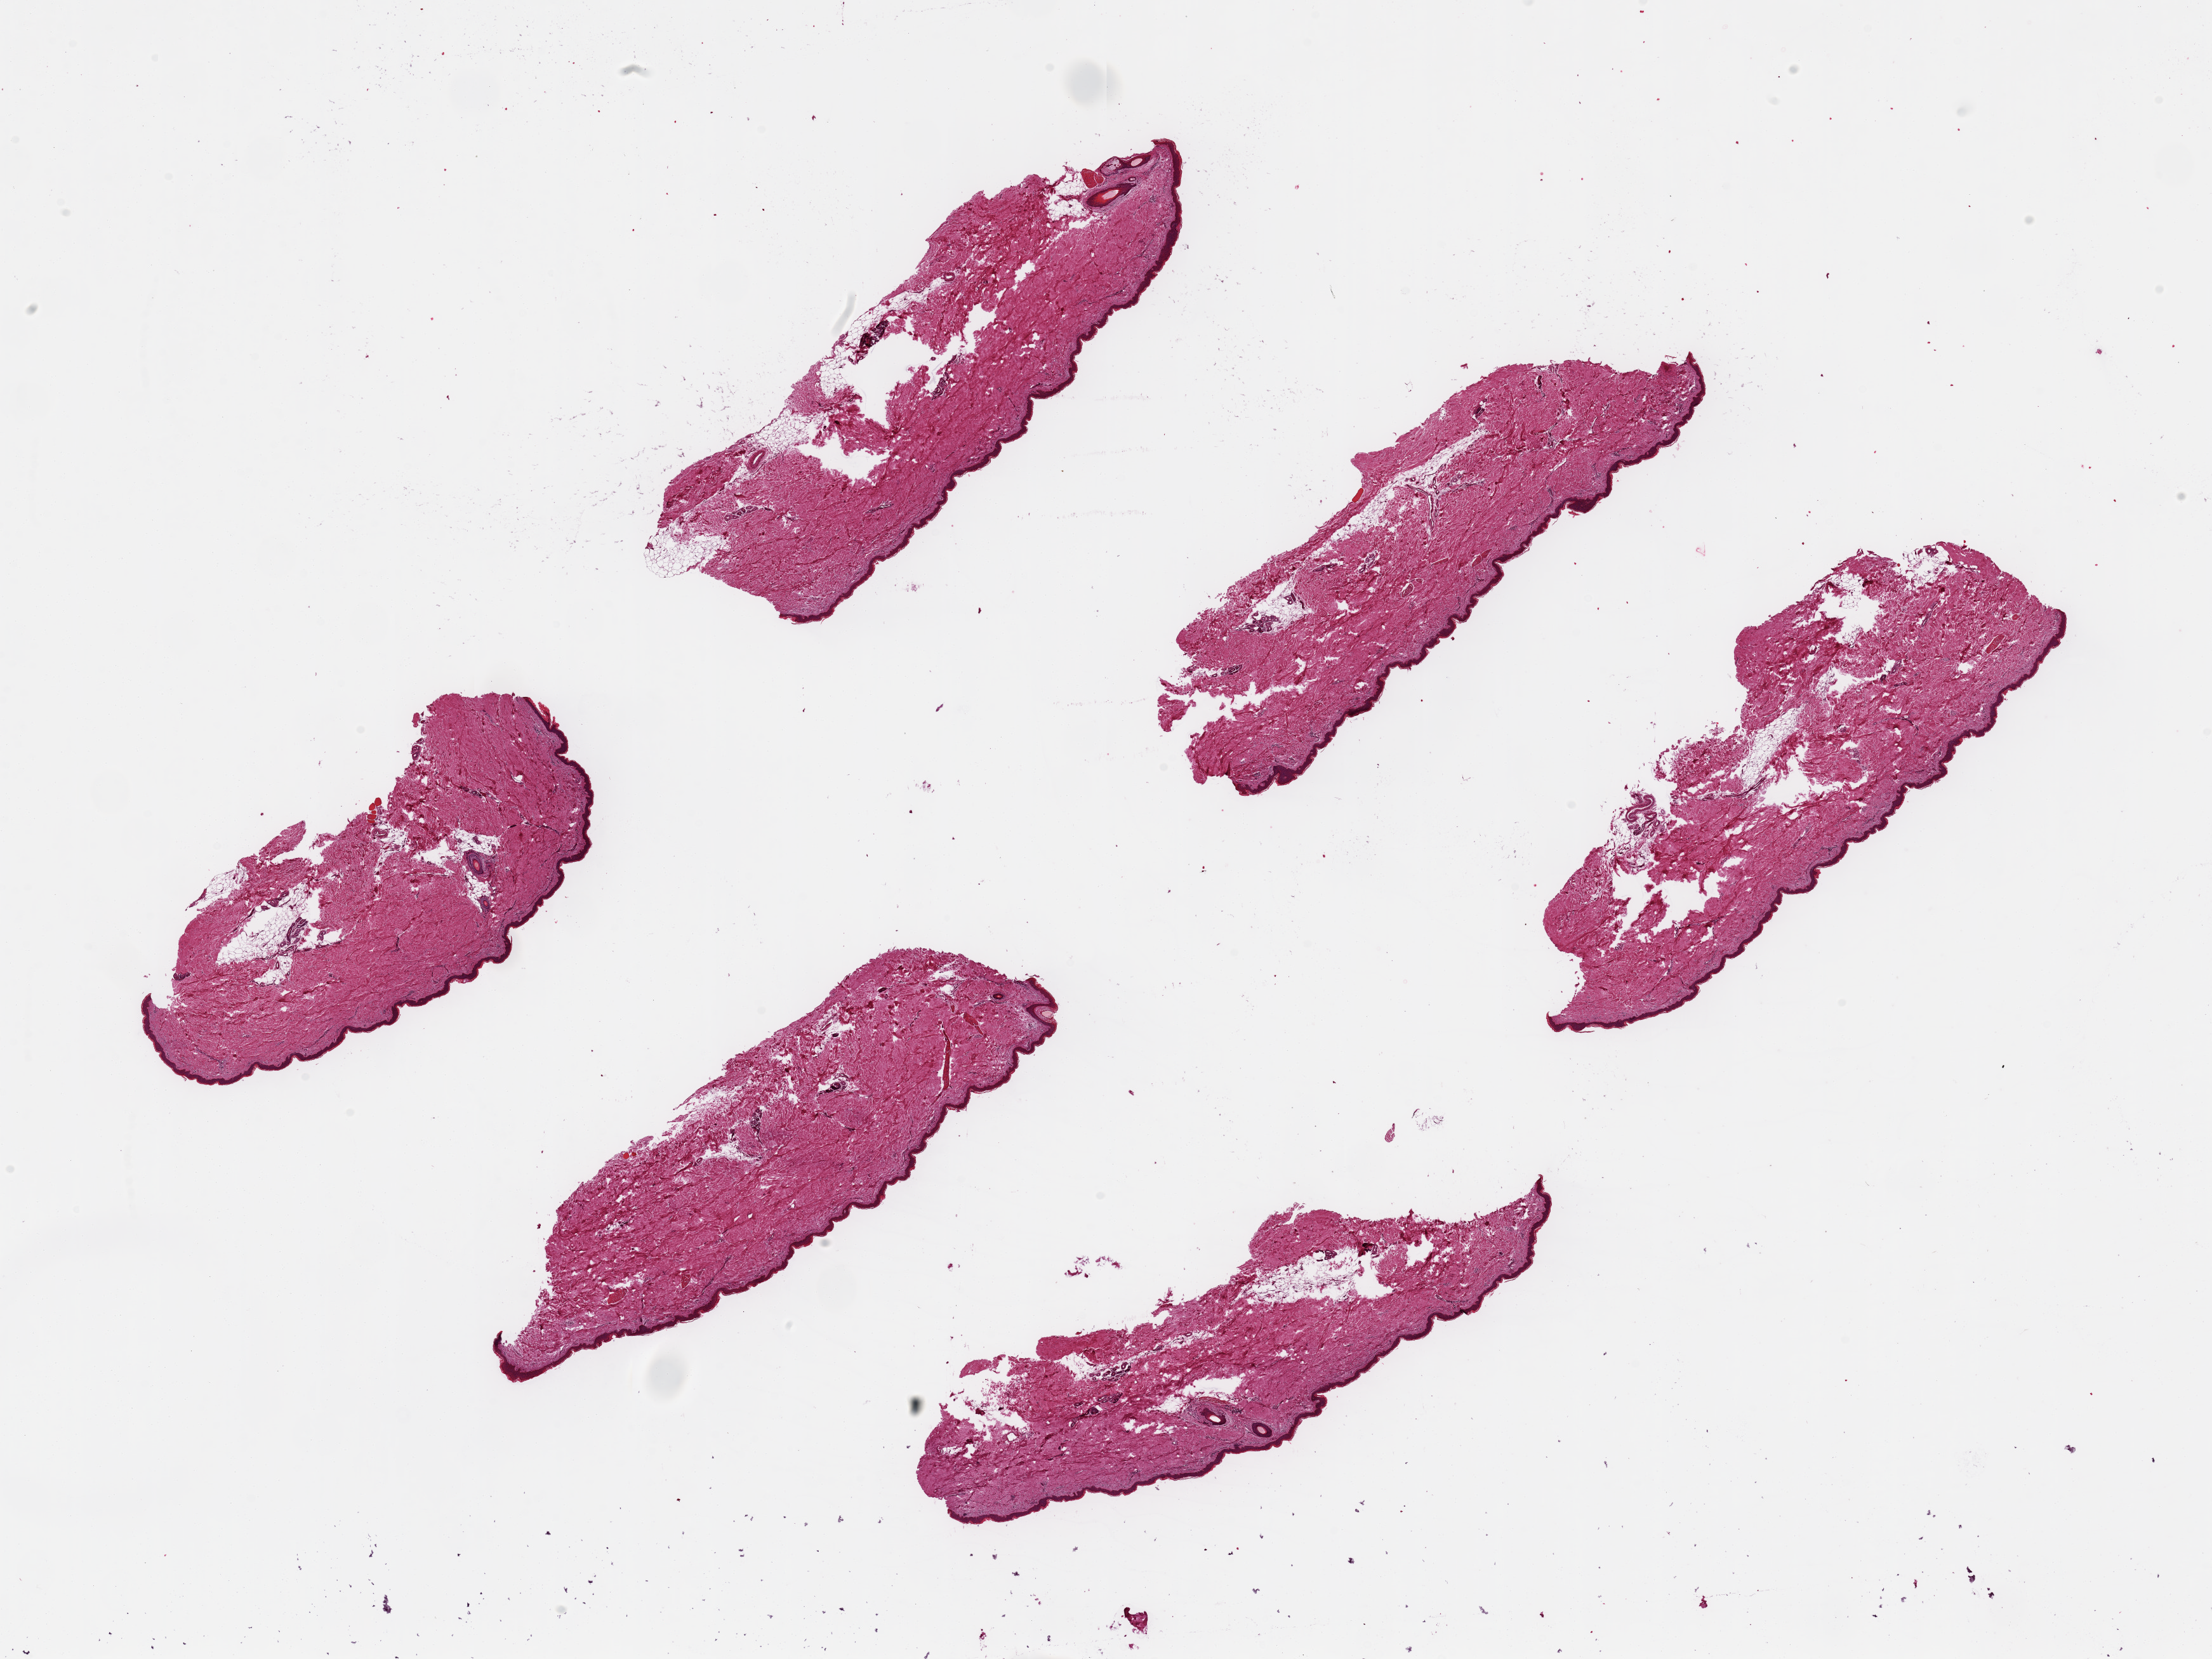
Whole-slide image, hematoxylin and eosin (H&E) stain — low-resolution overview of the scanned area, about 27.6 x 20.7 mm. PAXgene-fixed, paraffin-embedded tissue. Sampled site (target tissue): skin of lower leg. Donor tissue sample. Donor sex: male.
• pathologist's review note for this sample: 6 pieces up to 8x3 mm; moderate tissue tears